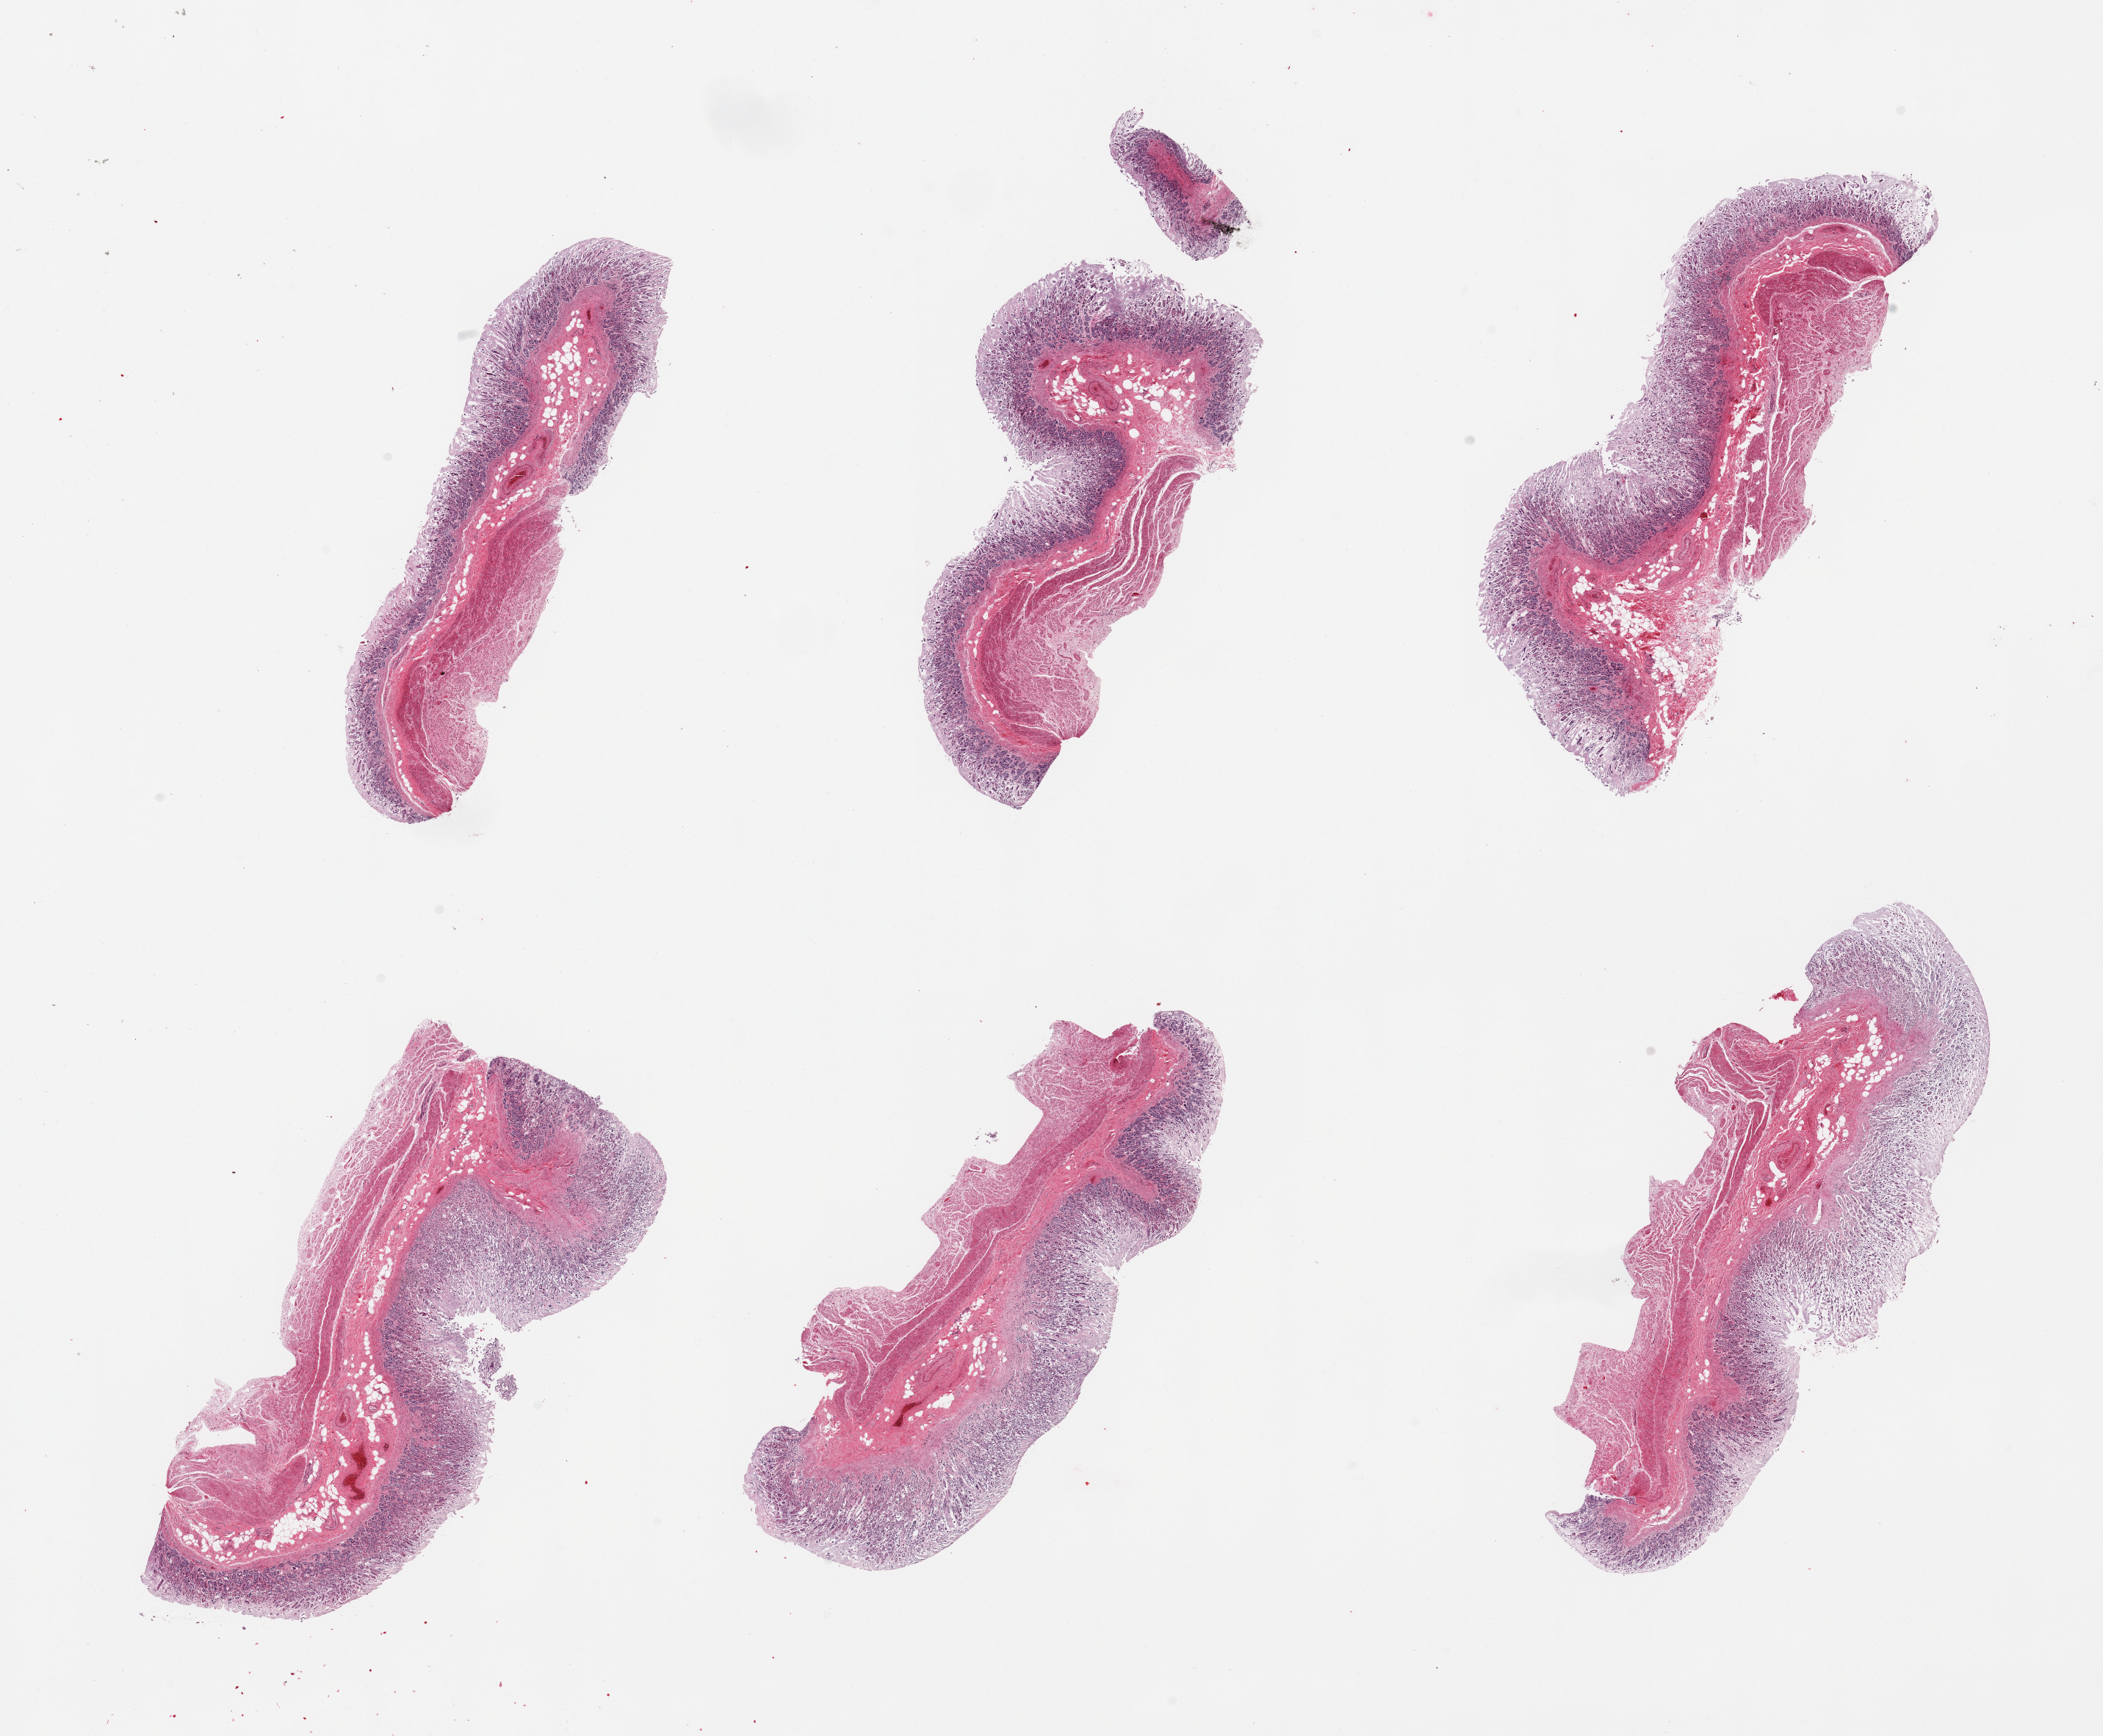
Hematoxylin and eosin (H&E) whole-slide image, a low-resolution overview of the entire scanned area, about 22.6 x 18.7 mm (from a 20x scan); PAXgene-fixed paraffin-embedded (PFPE) section; section of stomach (target tissue); tissue donor sample.
Review note (as recorded): 6 pieces; mucosa largely autolyzed; muscle in somewhat better shape.